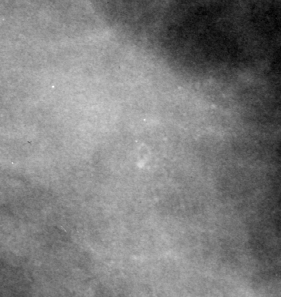
Cropped region of a digitized screen-film mammogram centred on a radiologist-marked abnormality, left breast, CC view.
Finding: calcifications, morphology pleomorphic, distribution clustered; BI-RADS assessment category 4; subtlety rating 2 on a 1 (subtle) to 5 (obvious) scale; pathology (as recorded): benign.